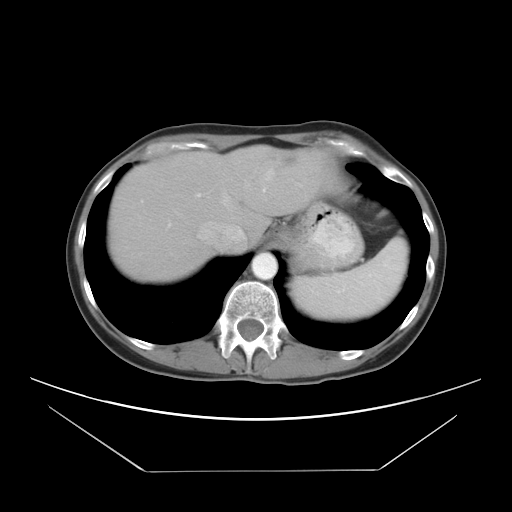
Contrast-enhanced abdominal CT, one axial slice; slice 24 of 30 in the series (ordered by position); intravenous contrast given; soft-tissue window (W 400 / L 40 HU); 7.5 mm slice thickness; 512 × 512 image matrix, field of view 412 × 412 mm. Female patient, age 54 years. From the clinical record (not read from this slice): diagnosis: colorectal cancer liver metastases, imaged before liver resection; multiple liver metastases: yes; largest metastasis: 2.5 cm; disease in both lobes: yes.
Outlined on this slice (manually delineated by an expert):
- hepatic veins: box from (x=199, y=169) to (x=274, y=242) px
- liver: (x=109, y=147)–(x=319, y=278)
- planned liver remnant (the part of the liver to remain after resection): (x=109, y=151)–(x=273, y=278)
- portal vein (with intrahepatic branches): (x=263, y=188)–(x=266, y=192)
- liver metastasis: (x=274, y=154)–(x=295, y=164)